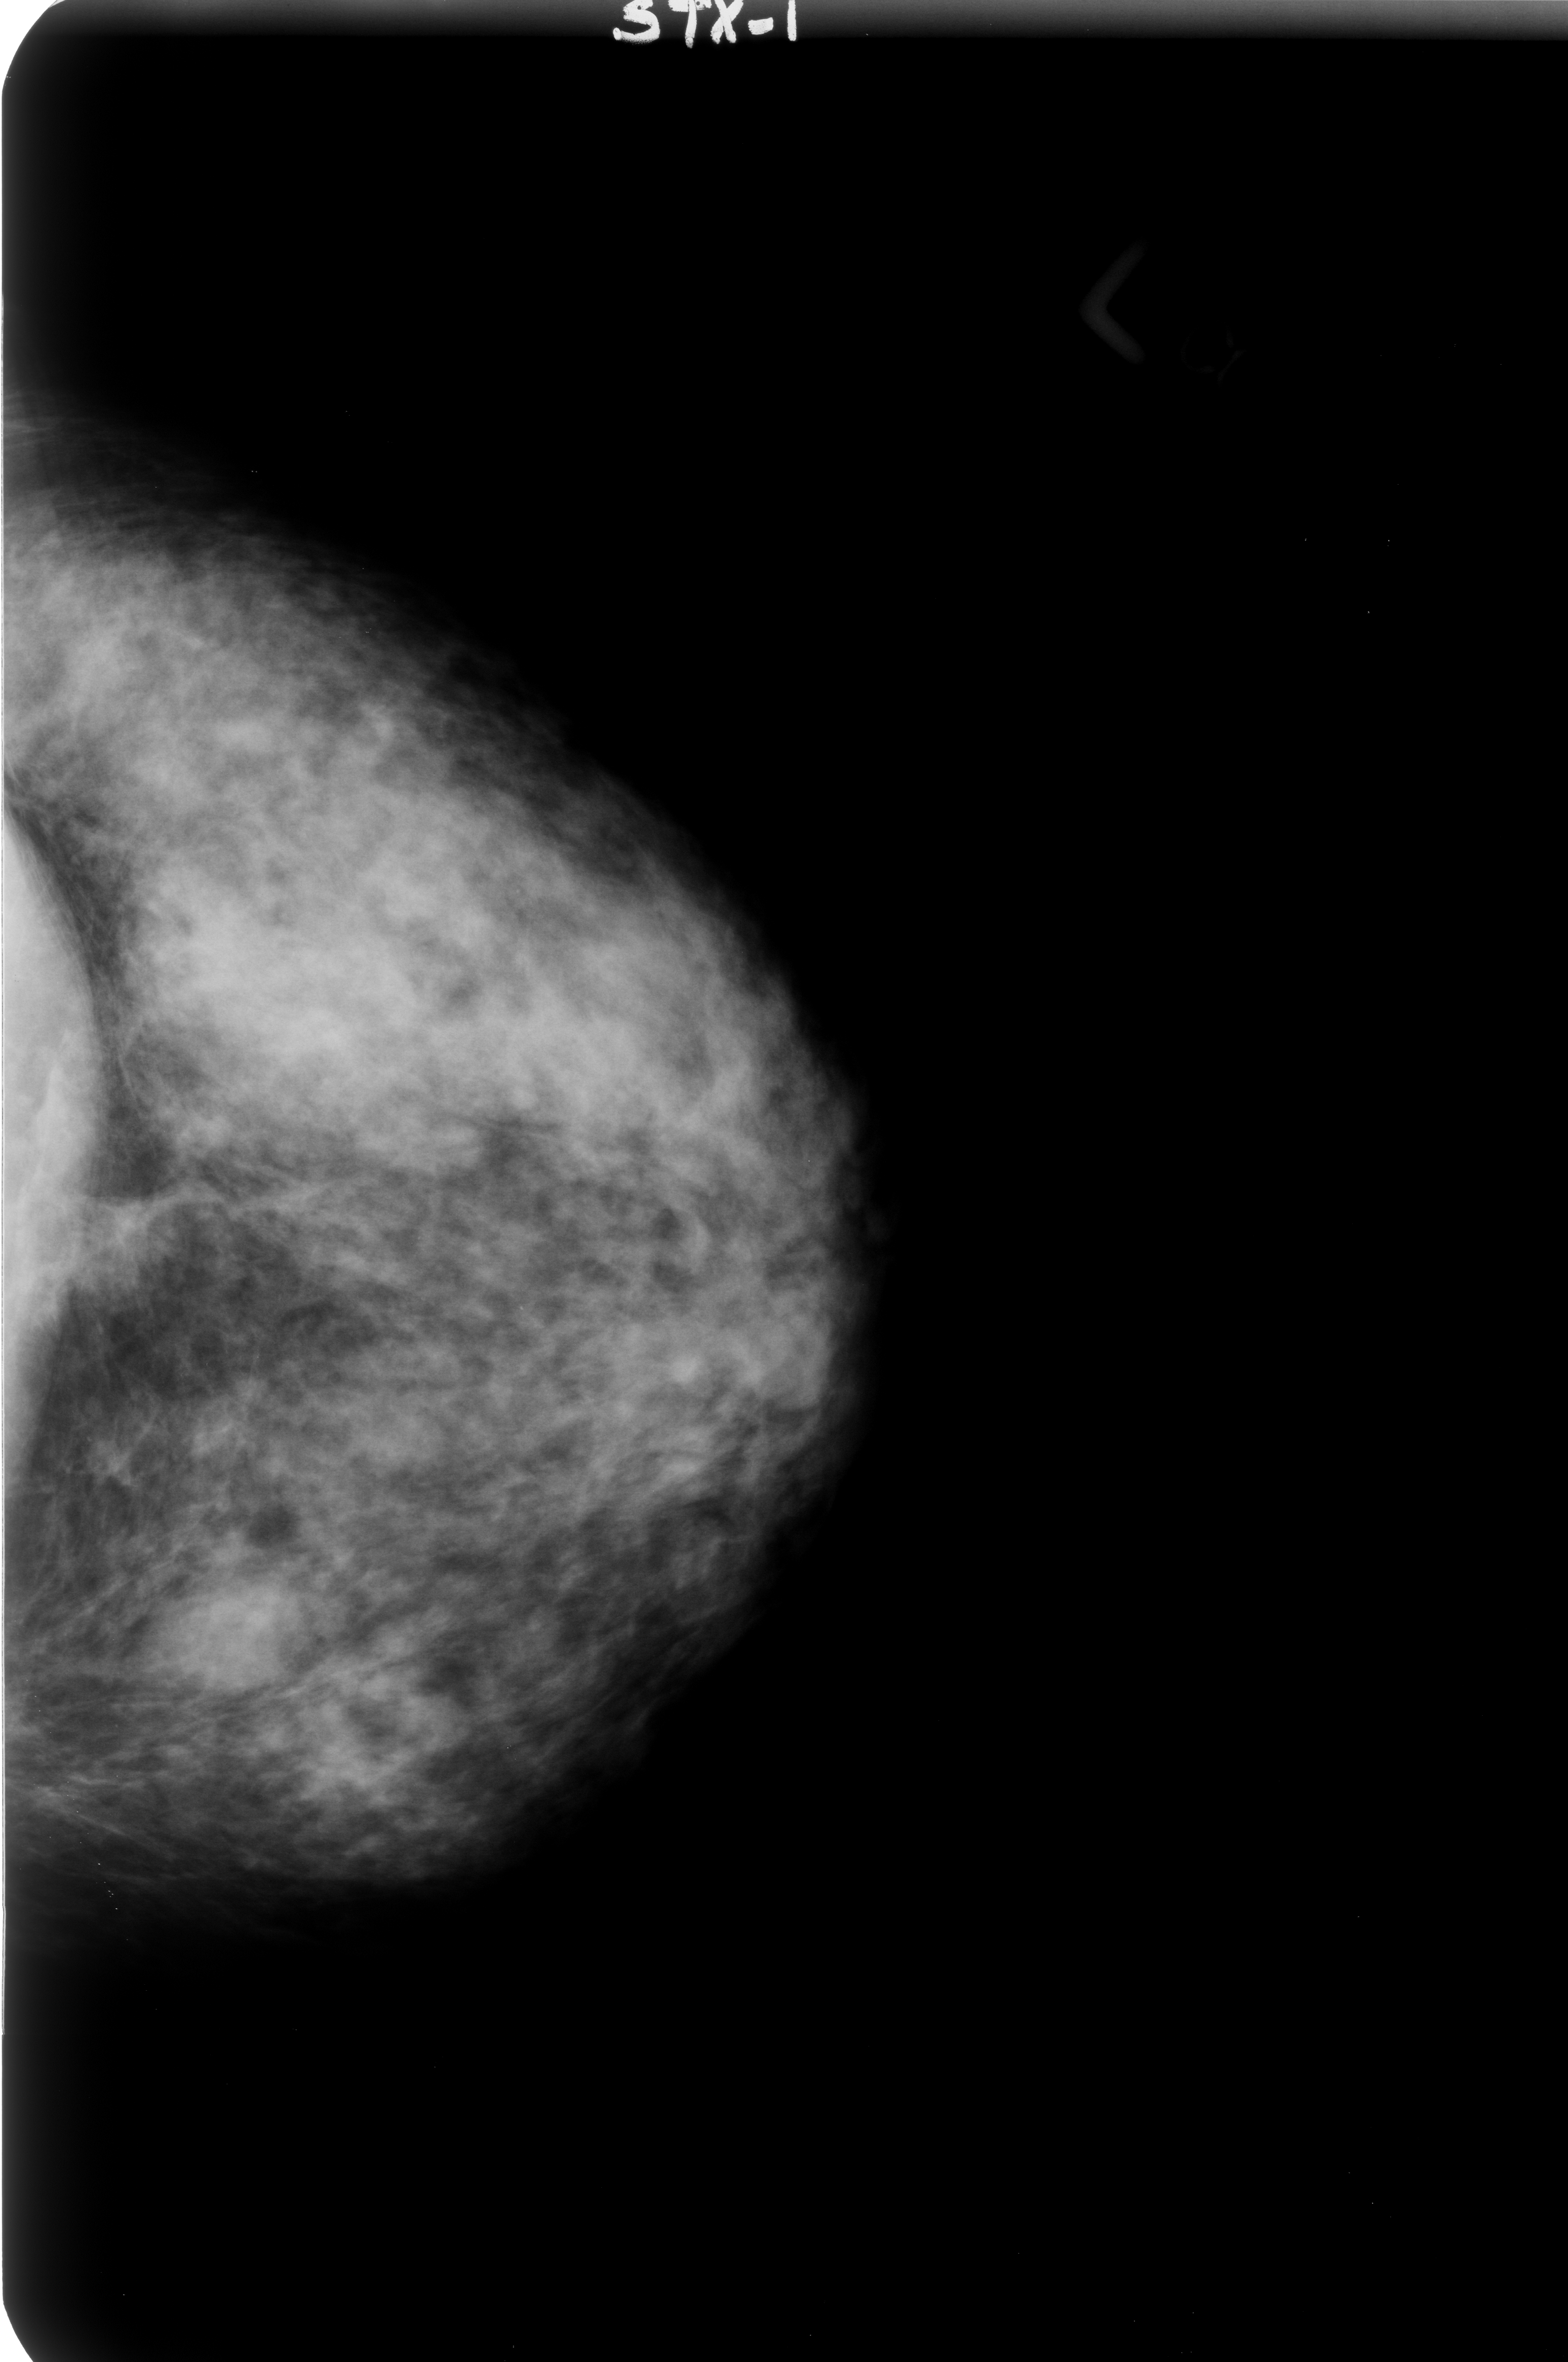
Scanned film-screen mammogram. Left breast. Craniocaudal (CC) view. Breast composition: heterogeneously dense (BI-RADS density category 3 of 4). 1568 × 2362 image matrix.
Expert-marked regions of interest on this film, with their recorded descriptors:
- mass, shape lobulated, margins circumscribed; BI-RADS assessment category 3; subtlety rating 3 on a 1 (subtle) to 5 (obvious) scale; pathology result (as recorded, not read from the image): benign: box from (x=150, y=1572) to (x=302, y=1691) px